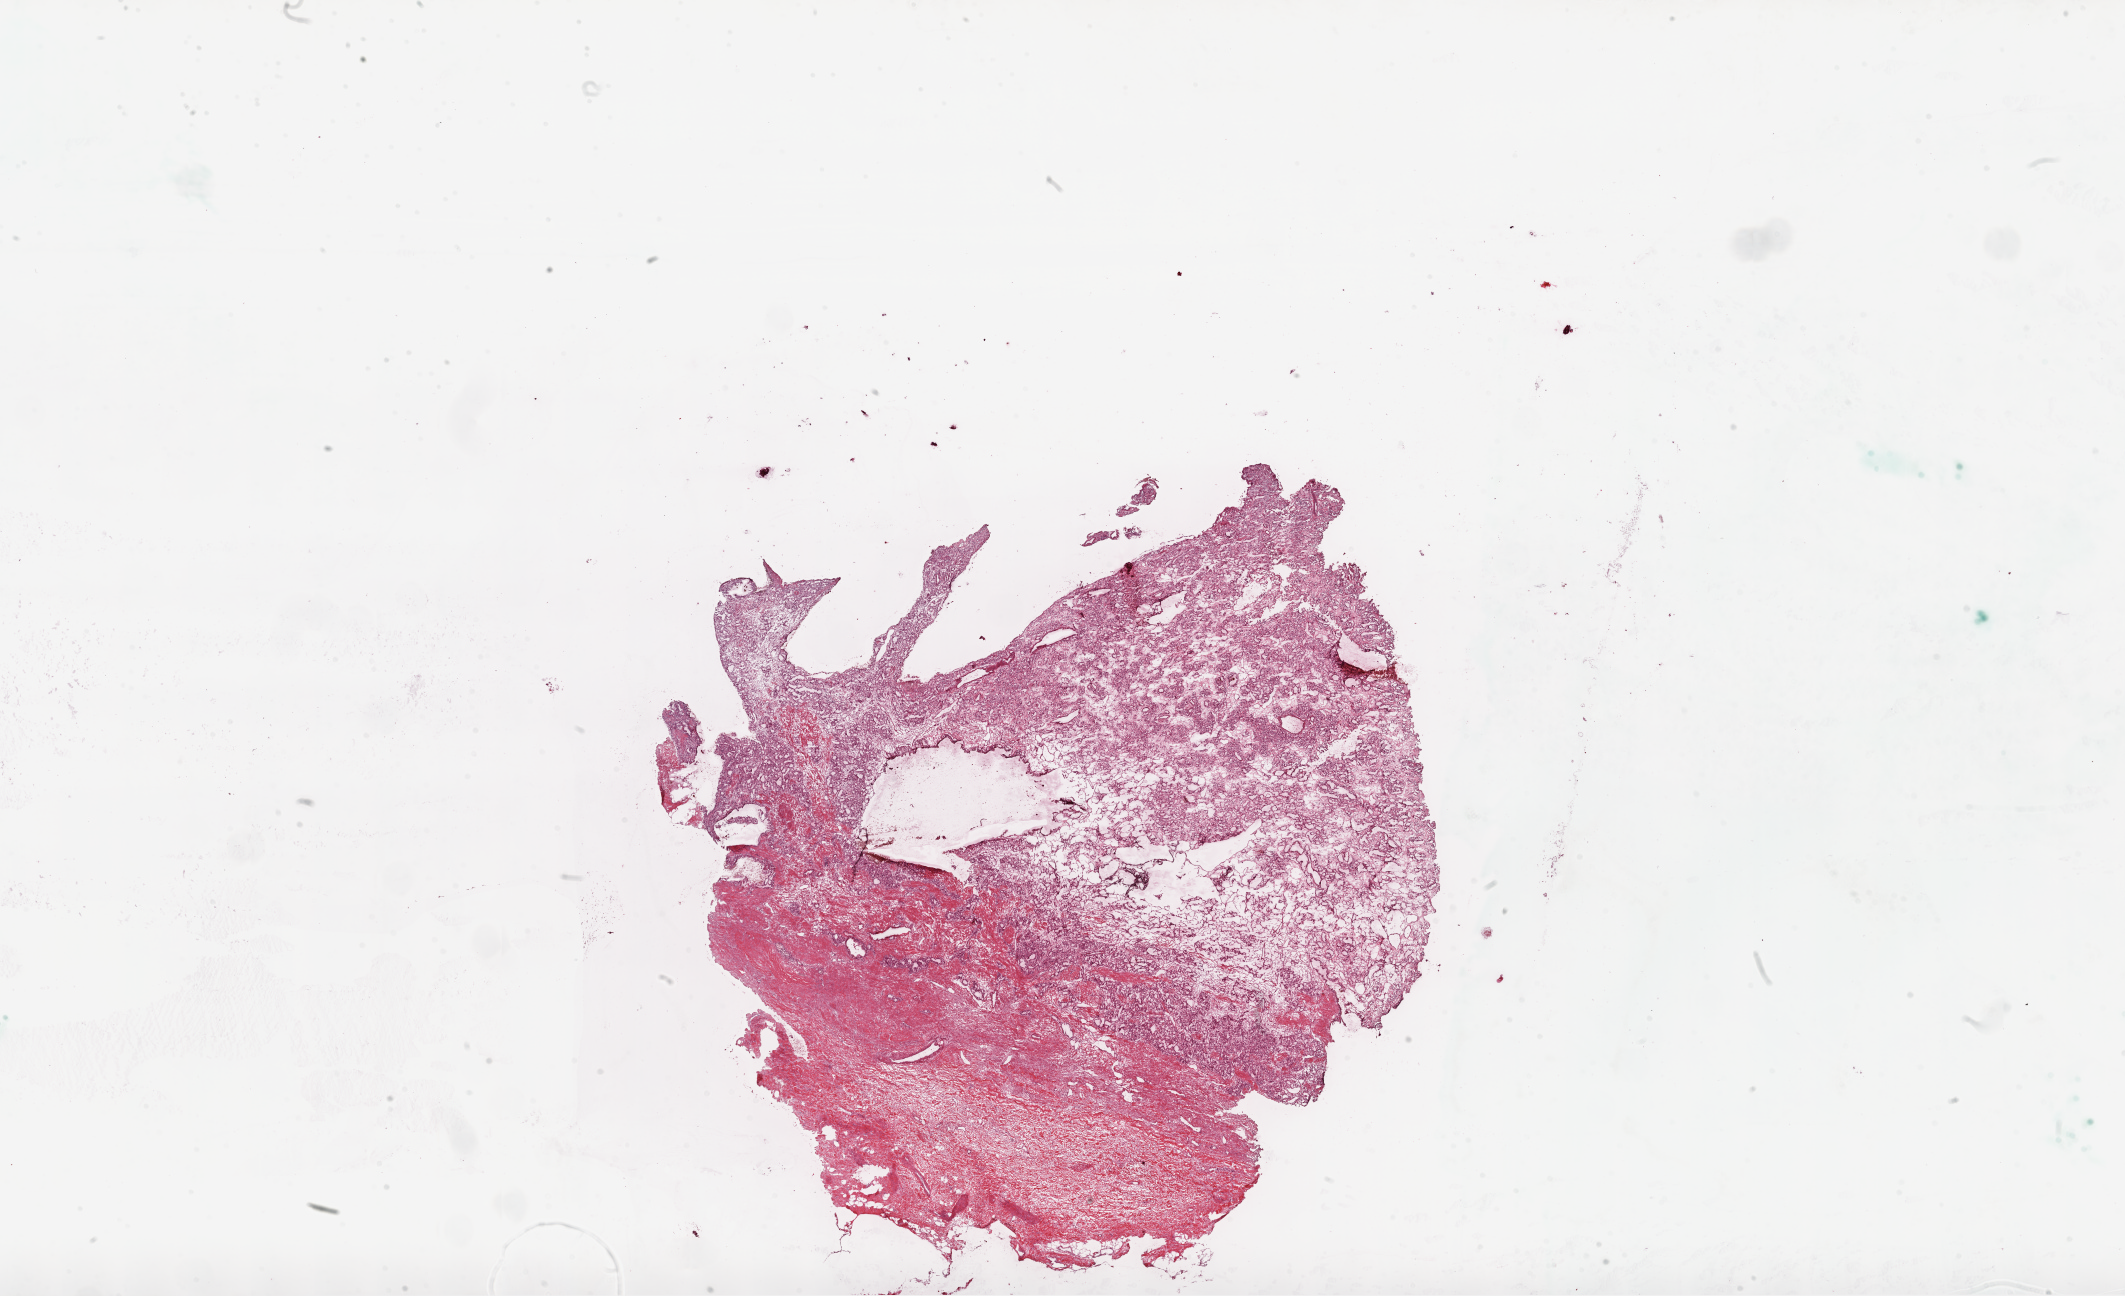
H&E-stained whole-slide image — a low-resolution overview of the entire scanned area, about 34.1 x 20.8 mm. Frozen section from the top of the tissue portion. Sample: primary tumour, kidney. Male, age 63 years at initial diagnosis. Histologic grade: G2 (moderately differentiated). Composition of this section per pathologist review: tumour cells 60%, tumour nuclei 80%, normal cells 0%, stromal cells 40%, necrosis 0%.
- AJCC pathologic stage: I
- diagnosis: Clear cell adenocarcinoma, NOS
- laterality: left